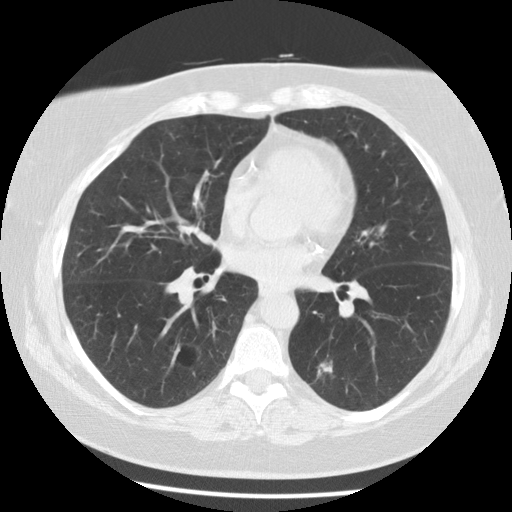
Low-dose screening chest CT, one axial slice; slice 55 of 116 in the series (ordered by position); reconstruction kernel STANDARD; lung window (W 1500 / L -600 HU); 2.5 mm slice thickness; 512 × 512 image matrix, field of view 341 × 341 mm.
Annotated regions visible in this slice (outlined manually by an expert reader):
- lesion 1 (tumor, lower lobe of left lung): bounding box <318,363,332,374> (left, top, right, bottom; pixels)